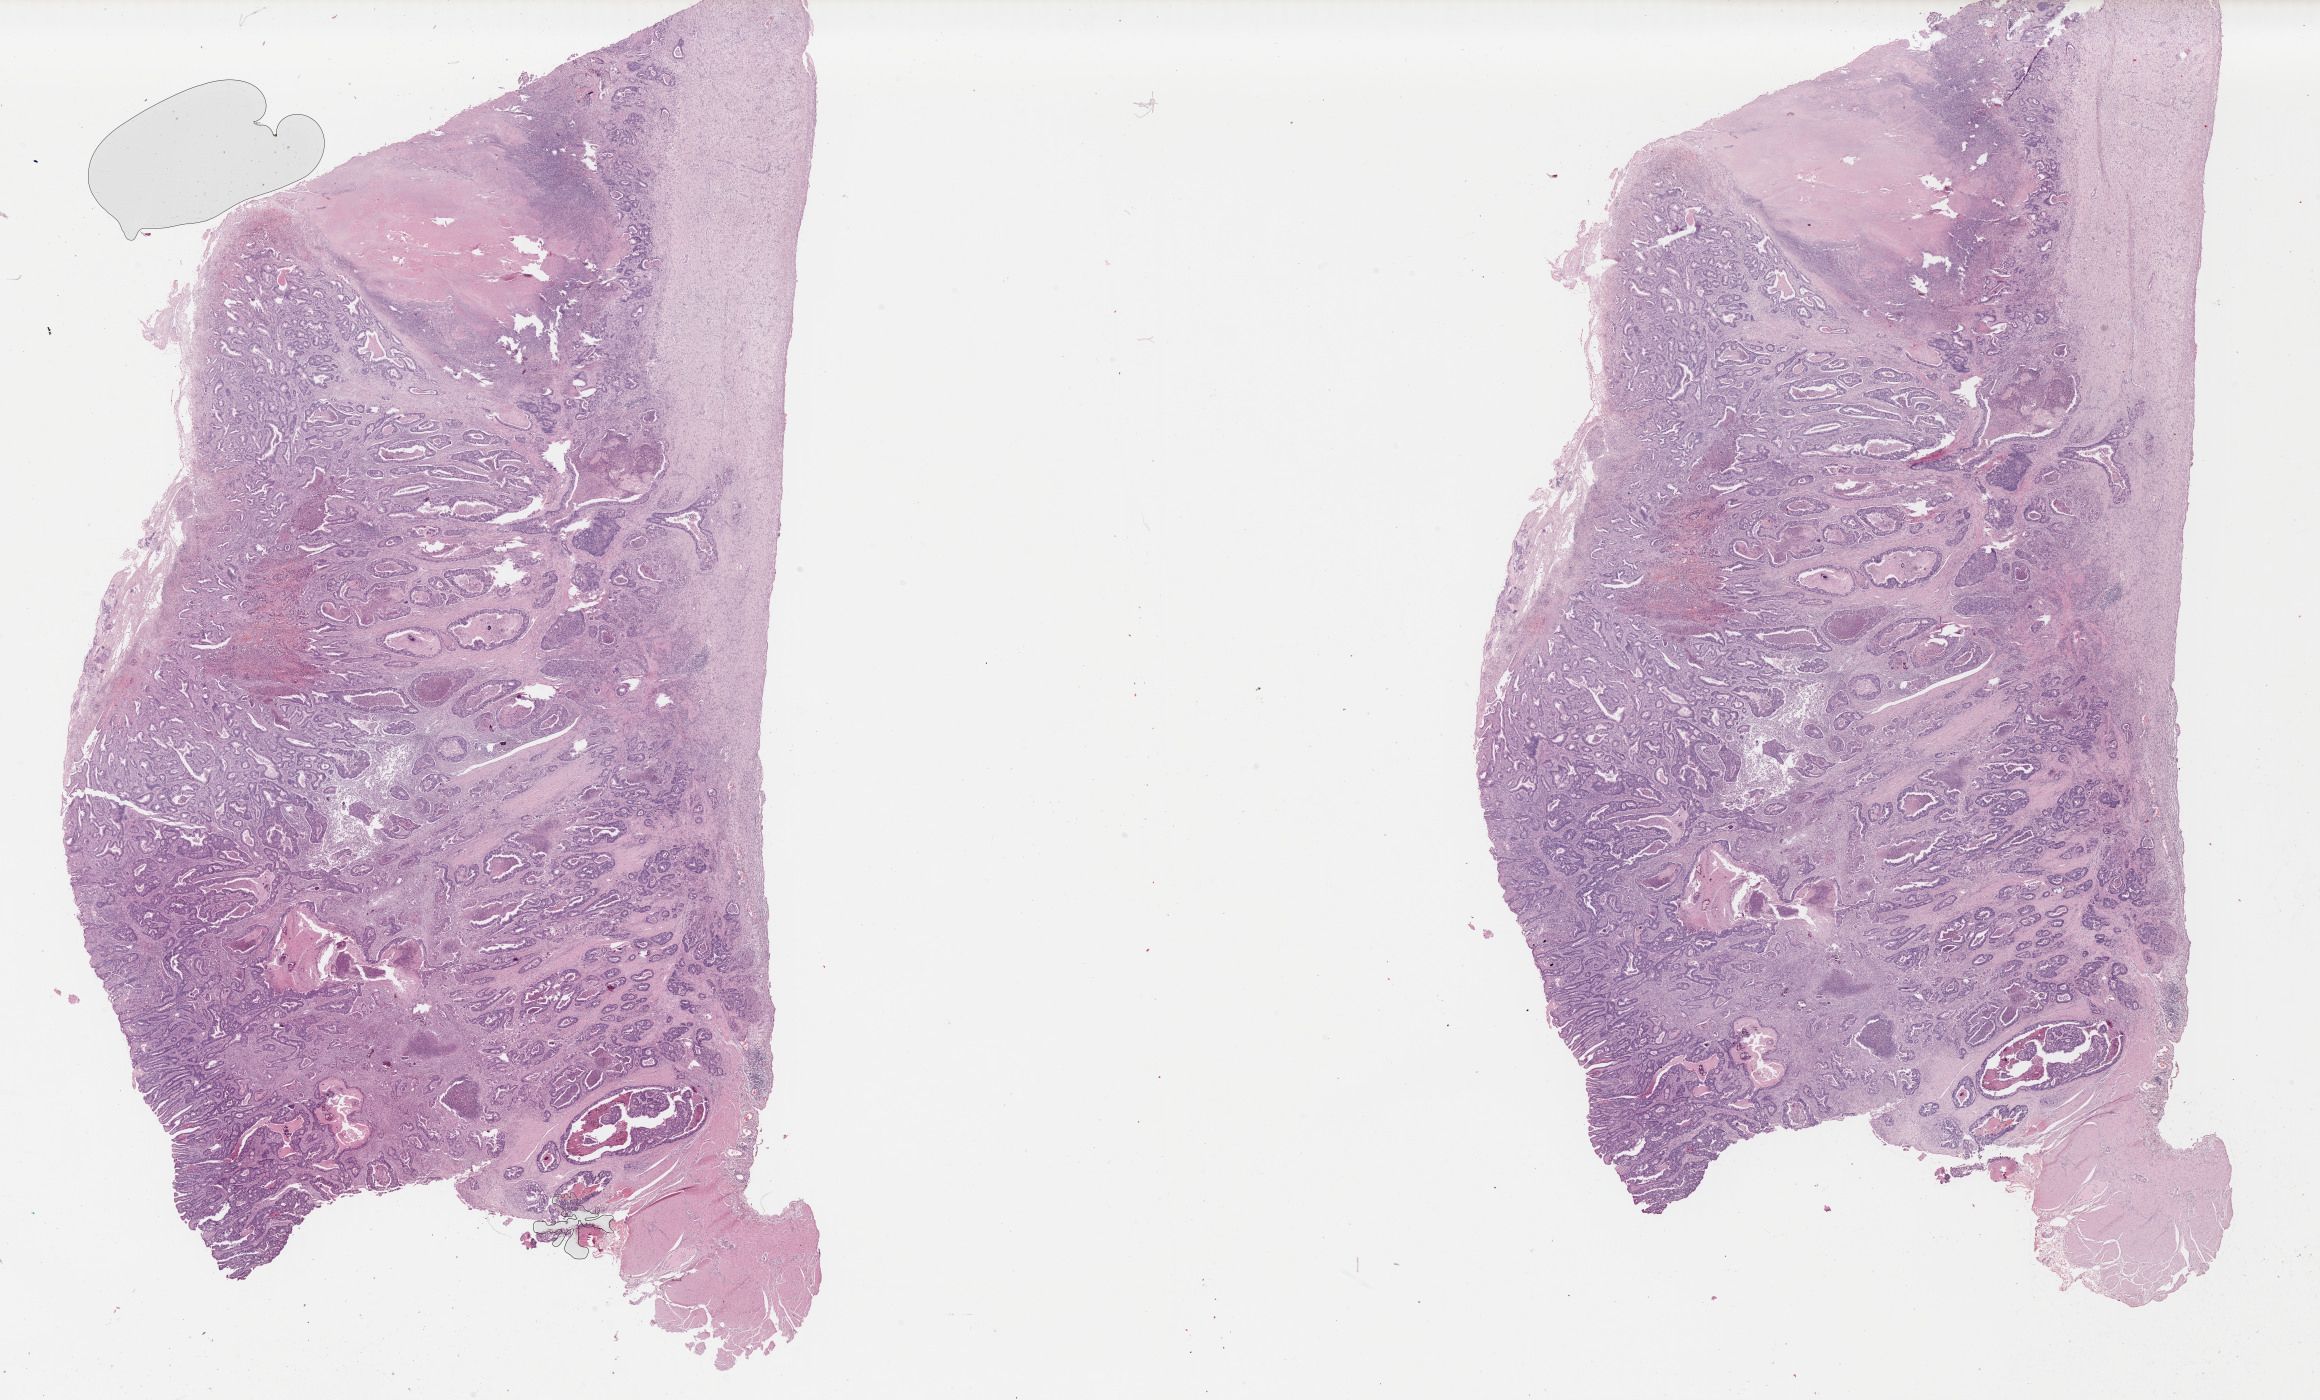
Digitized H&E-stained tissue section (whole slide) — a low-resolution overview of the entire scanned area, about 36.5 x 22.0 mm (acquisition: 40x scan). Formalin-fixed paraffin-embedded (FFPE) diagnostic section. Stomach, primary tumour sample. Female, age 70 years at initial diagnosis. Histologic grade: G2 (moderately differentiated).
Lymph nodes positive (case pathology): 5 of 19 examined. Pathologic diagnosis: Tubular adenocarcinoma (body of stomach). AJCC pathologic stage: IIB.